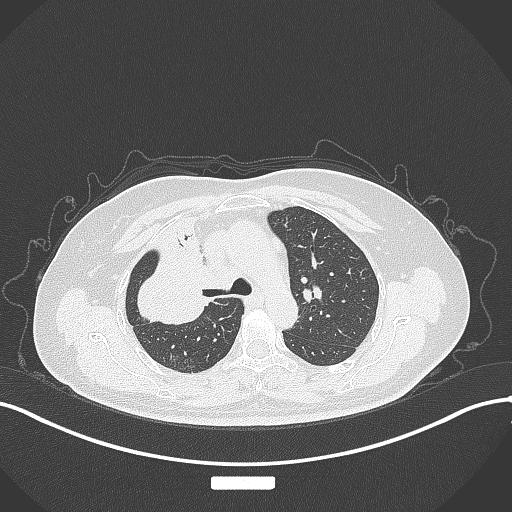
Chest CT, one axial slice; position 218 of 309 along the scan axis; reconstruction kernel B70f; lung window (W 1500 / L -600 HU); 1 mm slice thickness; 512 × 512 image matrix, field of view 400 × 400 mm. Patient: female, 60 years. Case-level facts recorded for this patient, not image findings: clinical TNM (as recorded): T3 N1 M1.
Structures marked on this image (bounding box drawn by a radiologist):
- lung tumour (recorded histology: adenocarcinoma): bounding box (x1, y1, x2, y2) in pixels: (128, 228, 213, 331)